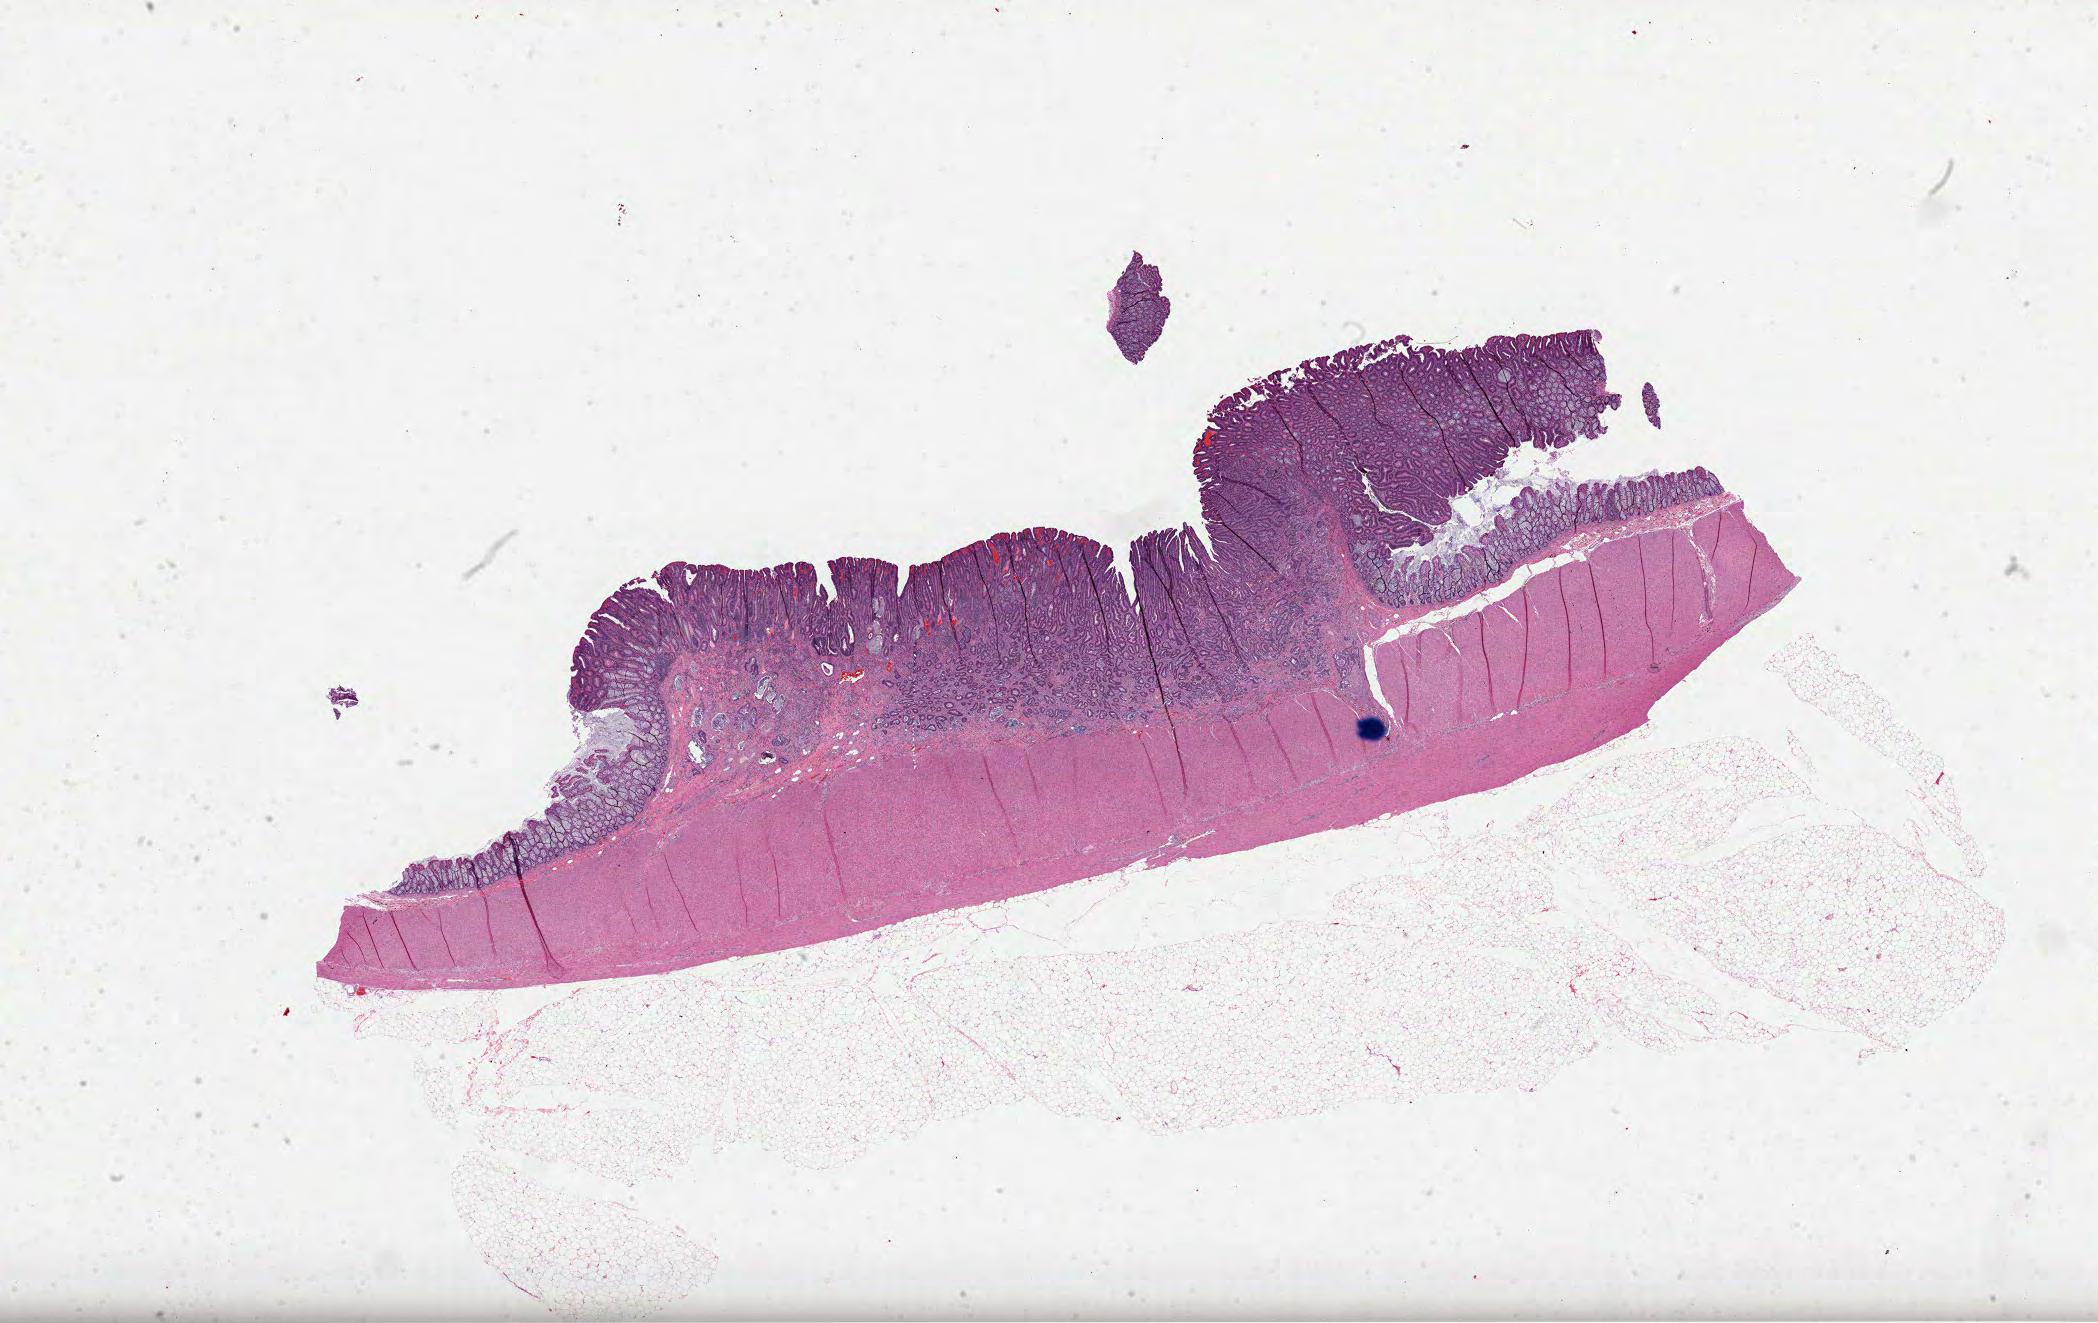
Whole-slide histology image, H&E-stained — shown as a low-resolution overview of the whole scanned area (about 33.8 x 21.3 mm, slide scanned at 40x); formalin-fixed paraffin-embedded (FFPE) diagnostic section; primary tumour sample from the colon. Female patient; age at initial diagnosis 72 years.
Pathologic diagnosis: Adenocarcinoma, NOS (descending colon). TNM: T2 N0 M0. AJCC pathologic stage: I (7th edition).